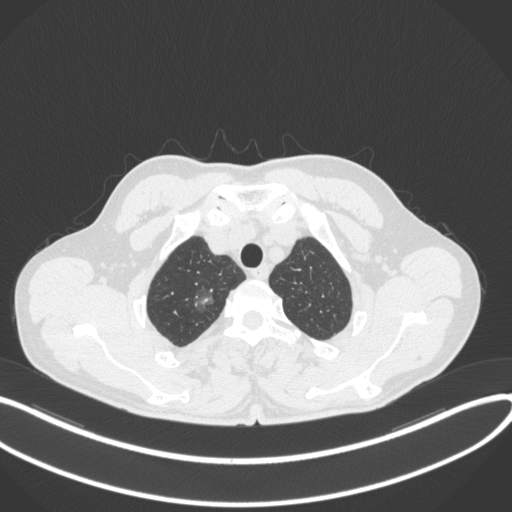
Chest CT, one axial slice. Position 333 of 407 along the scan axis. 120 kVp. Lung window (W 1500 / L -600 HU). 1 mm slice thickness. 512 × 512 image matrix, field of view 400 × 400 mm. Male patient, age 58 years. From the clinical record (not read from this slice): clinical TNM (as recorded): T1c N0 M0; histopathological grade: G1-2.
Outlined on this slice (rectangle marked by the reading radiologist):
- lung tumour (recorded histology: adenocarcinoma): bounding box [x1, y1, x2, y2] px = [190, 286, 214, 312]